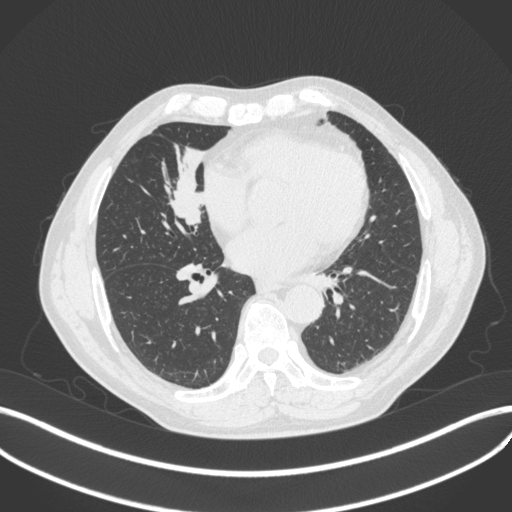
Chest CT, one axial slice; 120 kVp; lung window (W 1500 / L -600 HU); 512 × 512 image matrix, field of view 400 × 400 mm. Patient: male, 61 years. From the clinical record (not read from this slice): clinical TNM (as recorded): T2b N1 M0.
Annotated regions visible in this slice (bounding box drawn by a radiologist):
- lung tumour (recorded histology: squamous cell carcinoma): box from (x=160, y=139) to (x=211, y=234) px